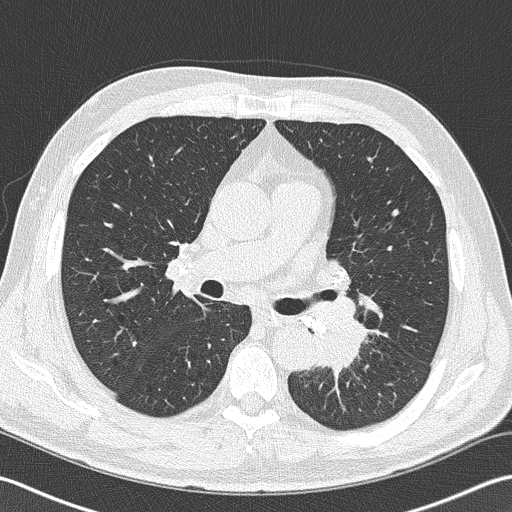
Chest CT (low-dose screening protocol), one axial image, second annual screen, lung window (W 1500 / L -600 HU), 2 mm slice thickness, slice 69 of 170 in the series, 512 × 512 image matrix. Male, age 57 years at enrolment.
Lesion marked by an expert reader, bounding box (x1, y1, x2, y2) in pixels: (294, 306, 374, 383). The exam's reader record, not a measurement of the box and not confirmed to be the same lesion: non-calcified nodule or mass ≥4 mm, left lower lobe, 40 × 30 mm, spiculated (stellate) margins, soft tissue attenuation, pre-existing on the prior screen: no. Official screen result: positive, other. Later outcome: lung cancer diagnosed 9 days after this screen — squamous cell carcinoma, NOS, left lower lobe, moderately differentiated (G2), stage IIIB (AJCC 6th edition), 38 mm at pathology.